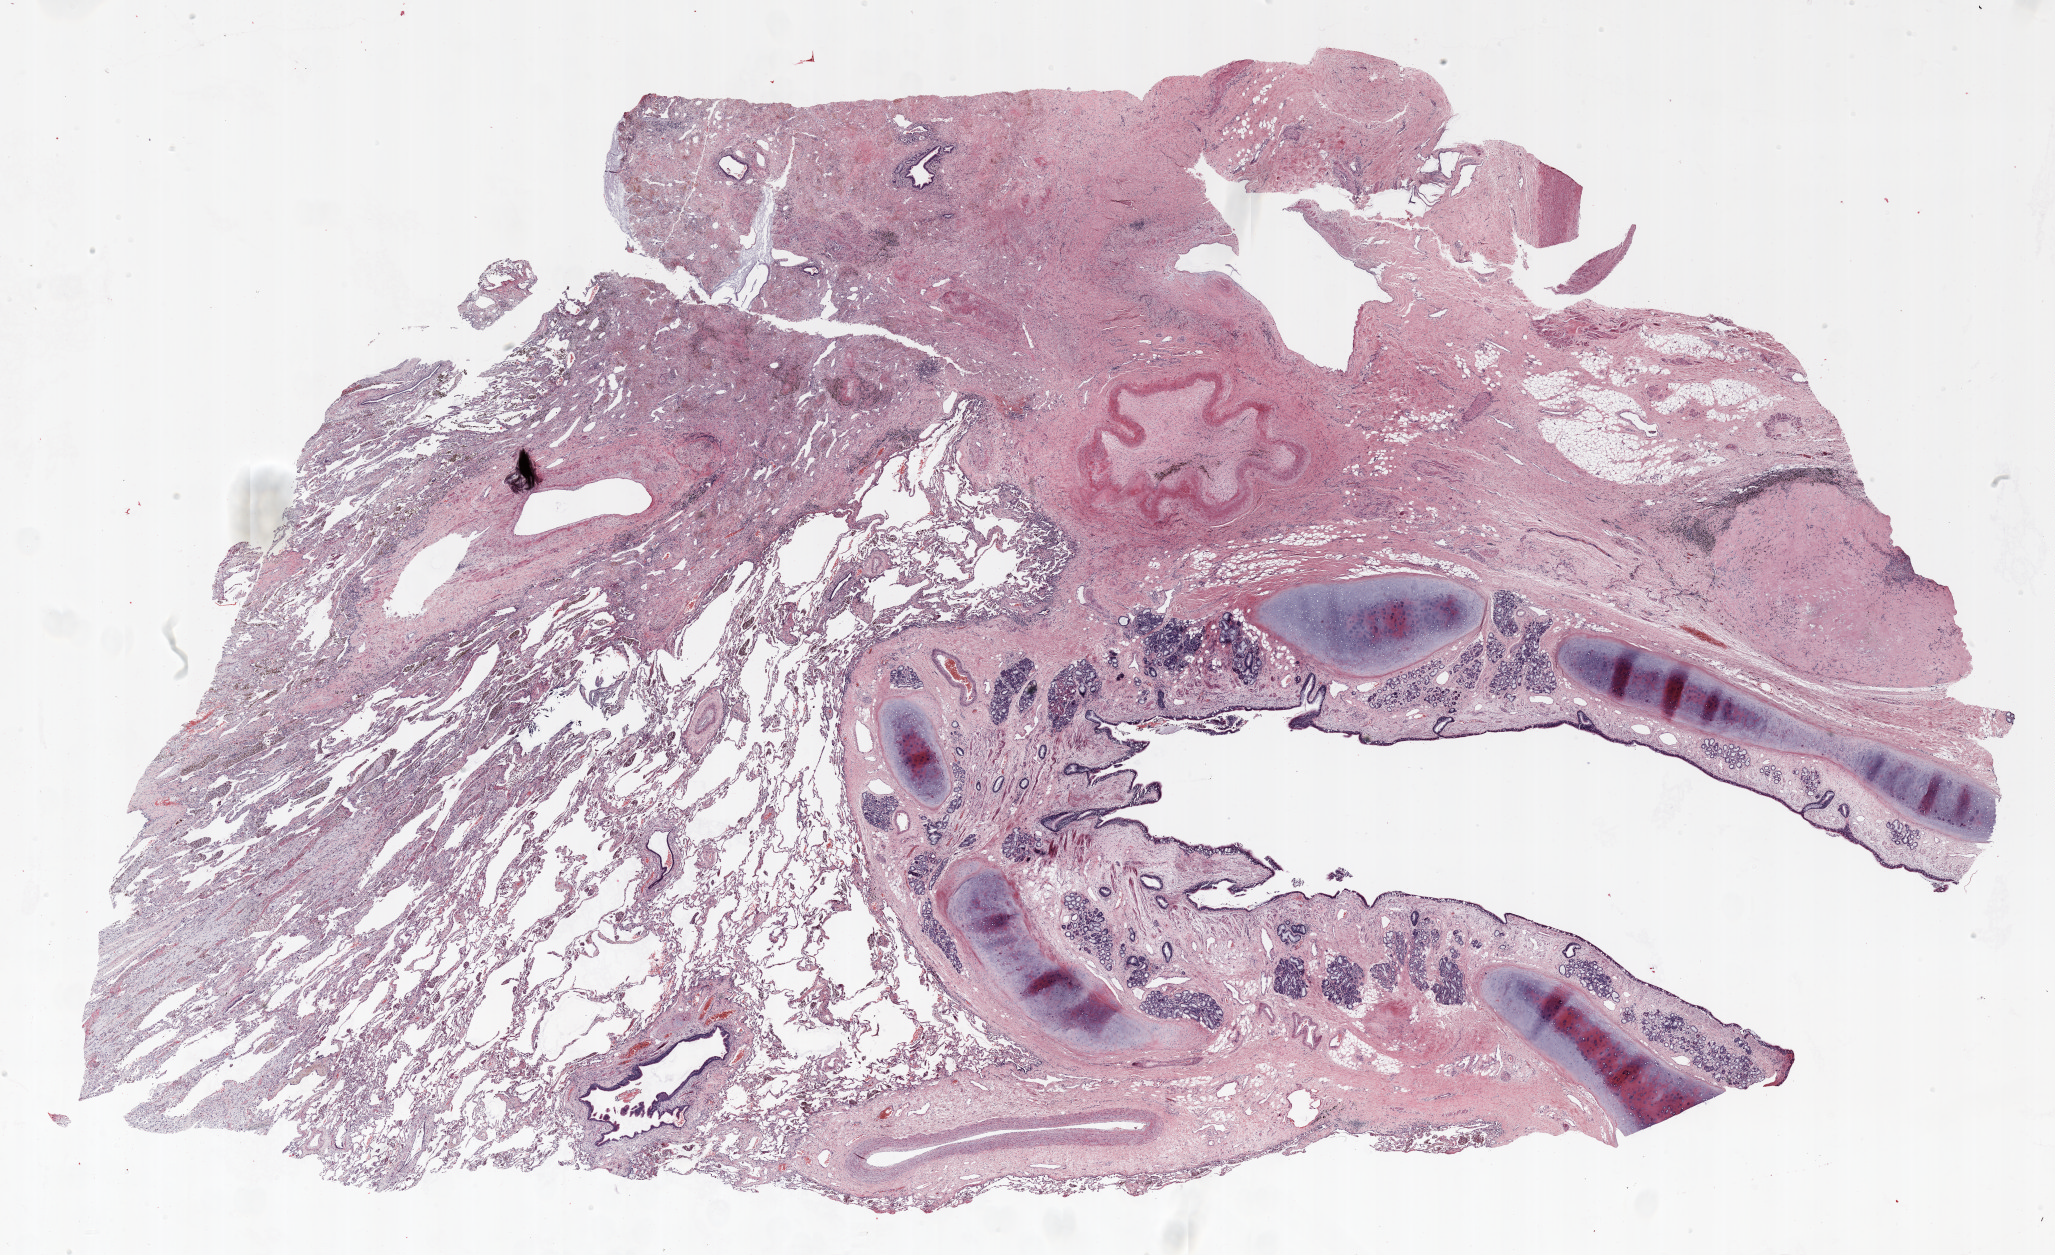
Whole-slide histology image, Hematoxylin and eosin (H&E) stained, shown as a low-resolution overview of the whole scanned area (about 33.0 x 20.2 mm, from a 20x scan). FFPE section. Lung tissue. Male patient, aged 58 at enrolment.
• primary tumour location (clinical record): right upper lobe, right hilum
• ICD-O-3 topography: overlapping lesion of lung (C34.8)
• participant's lung-cancer diagnosis: Non-small cell carcinoma
• stage (AJCC 6th edition): IB
• tumour size (pathology): 58 mm